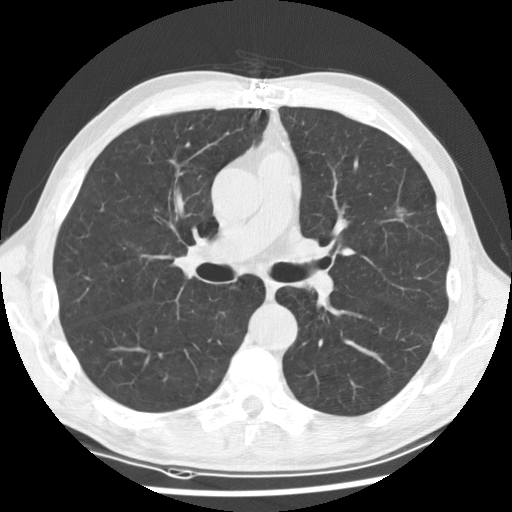
Chest CT (low-dose screening protocol), one axial image, first (baseline) screen, lung window (W 1500 / L -600 HU), 2.5 mm slice thickness. Male, age 64 years at enrolment. Current smoker at enrolment.
Lesion marked by an expert reader, bounding box [x1, y1, x2, y2] px = [376, 195, 431, 239]. Screening reader's record for this exam (one nodule recorded; not confirmed to be the boxed lesion): non-calcified nodule or mass ≥4 mm, left upper lobe, 13 × 10 mm, spiculated (stellate) margins, soft tissue attenuation.